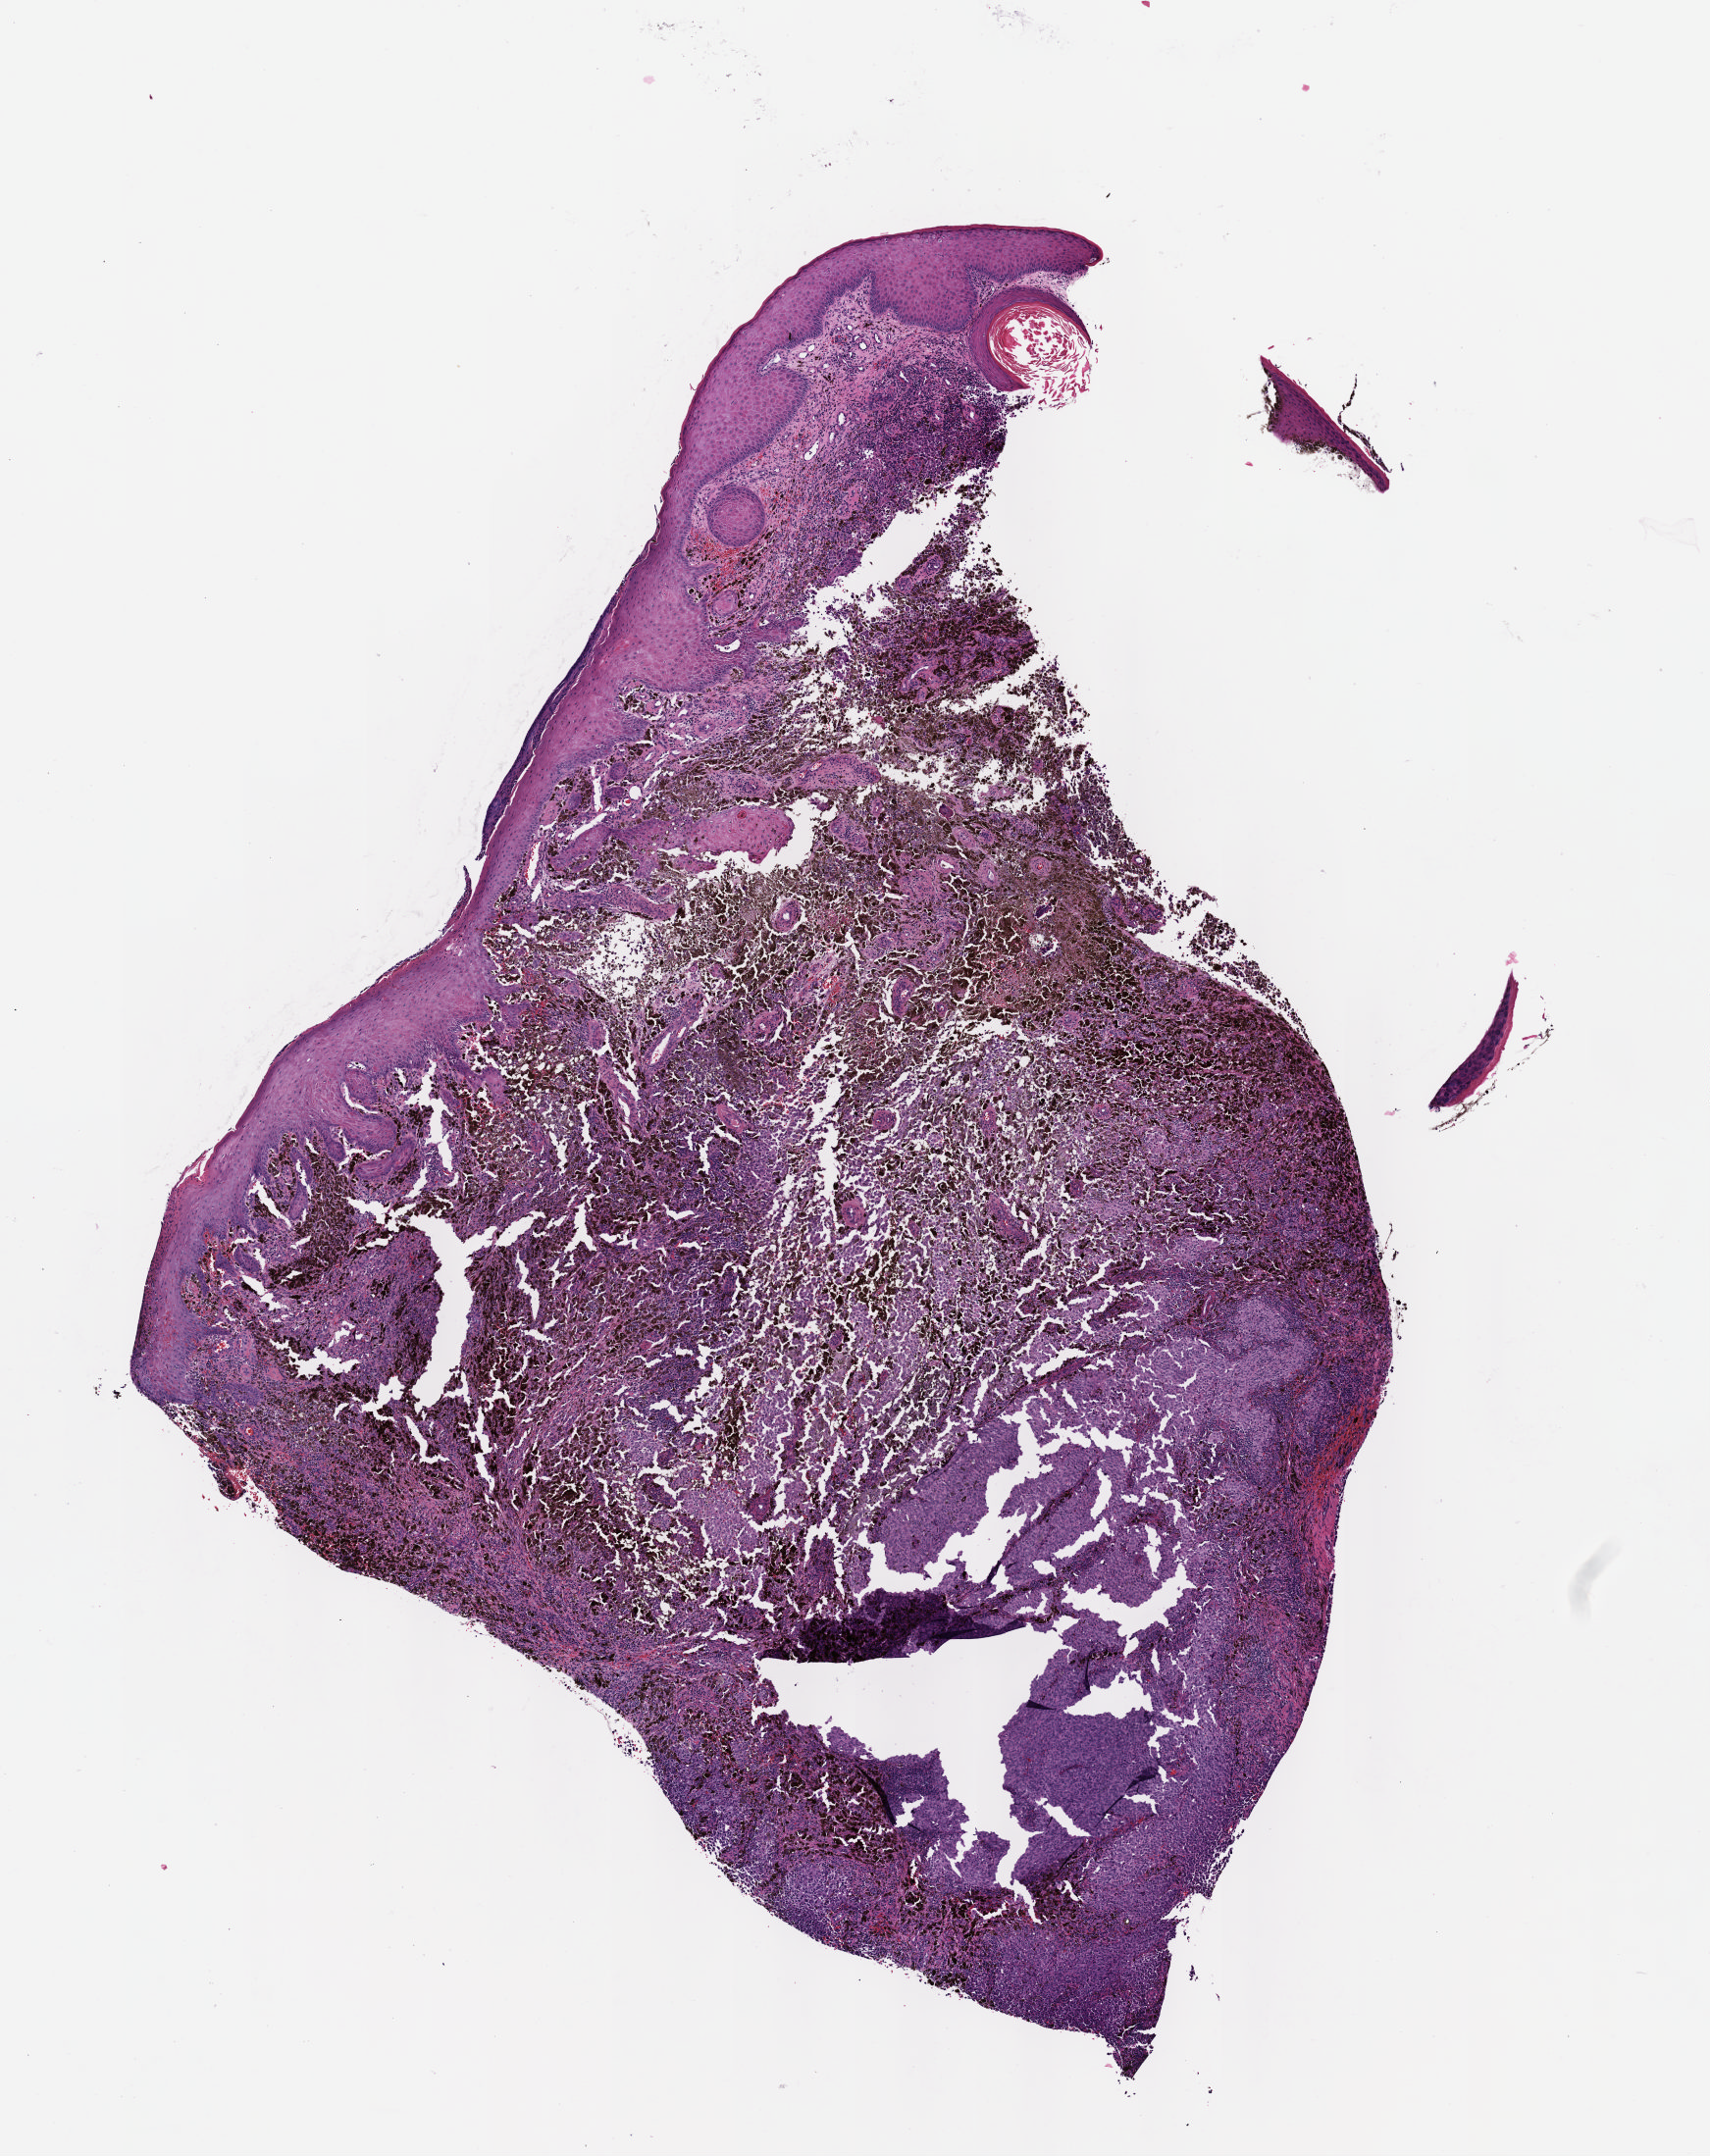
Whole-slide histology image, H&E, whole scanned area (about 7.0 x 8.9 mm, acquisition: 40x scan) shown as a low-resolution overview, formalin-fixed paraffin-embedded (FFPE) diagnostic section, primary tumour sample from the skin. Female, age 76 years at initial diagnosis.
Pathologic diagnosis: Epithelioid cell melanoma. AJCC pathologic stage: IIC (7th edition).